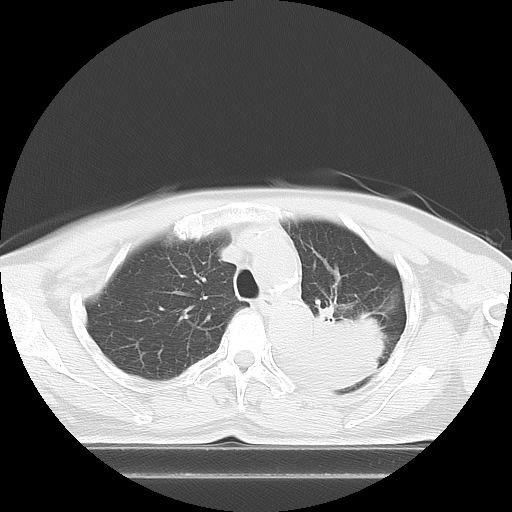
Chest CT, one axial slice; slice 8 of 21 in the series (ordered by position); 120 kVp; lung window (W 1500 / L -600 HU); 5 mm slice thickness; 512 × 512 image matrix. Patient: female, 74 years. From the clinical record (not read from this slice): clinical TNM (as recorded): T3 N1 M1c.
Outlined on this slice (rectangle marked by the reading radiologist):
- lung tumour (recorded histology: small cell carcinoma): bounding box <300,303,397,390> (left, top, right, bottom; pixels)